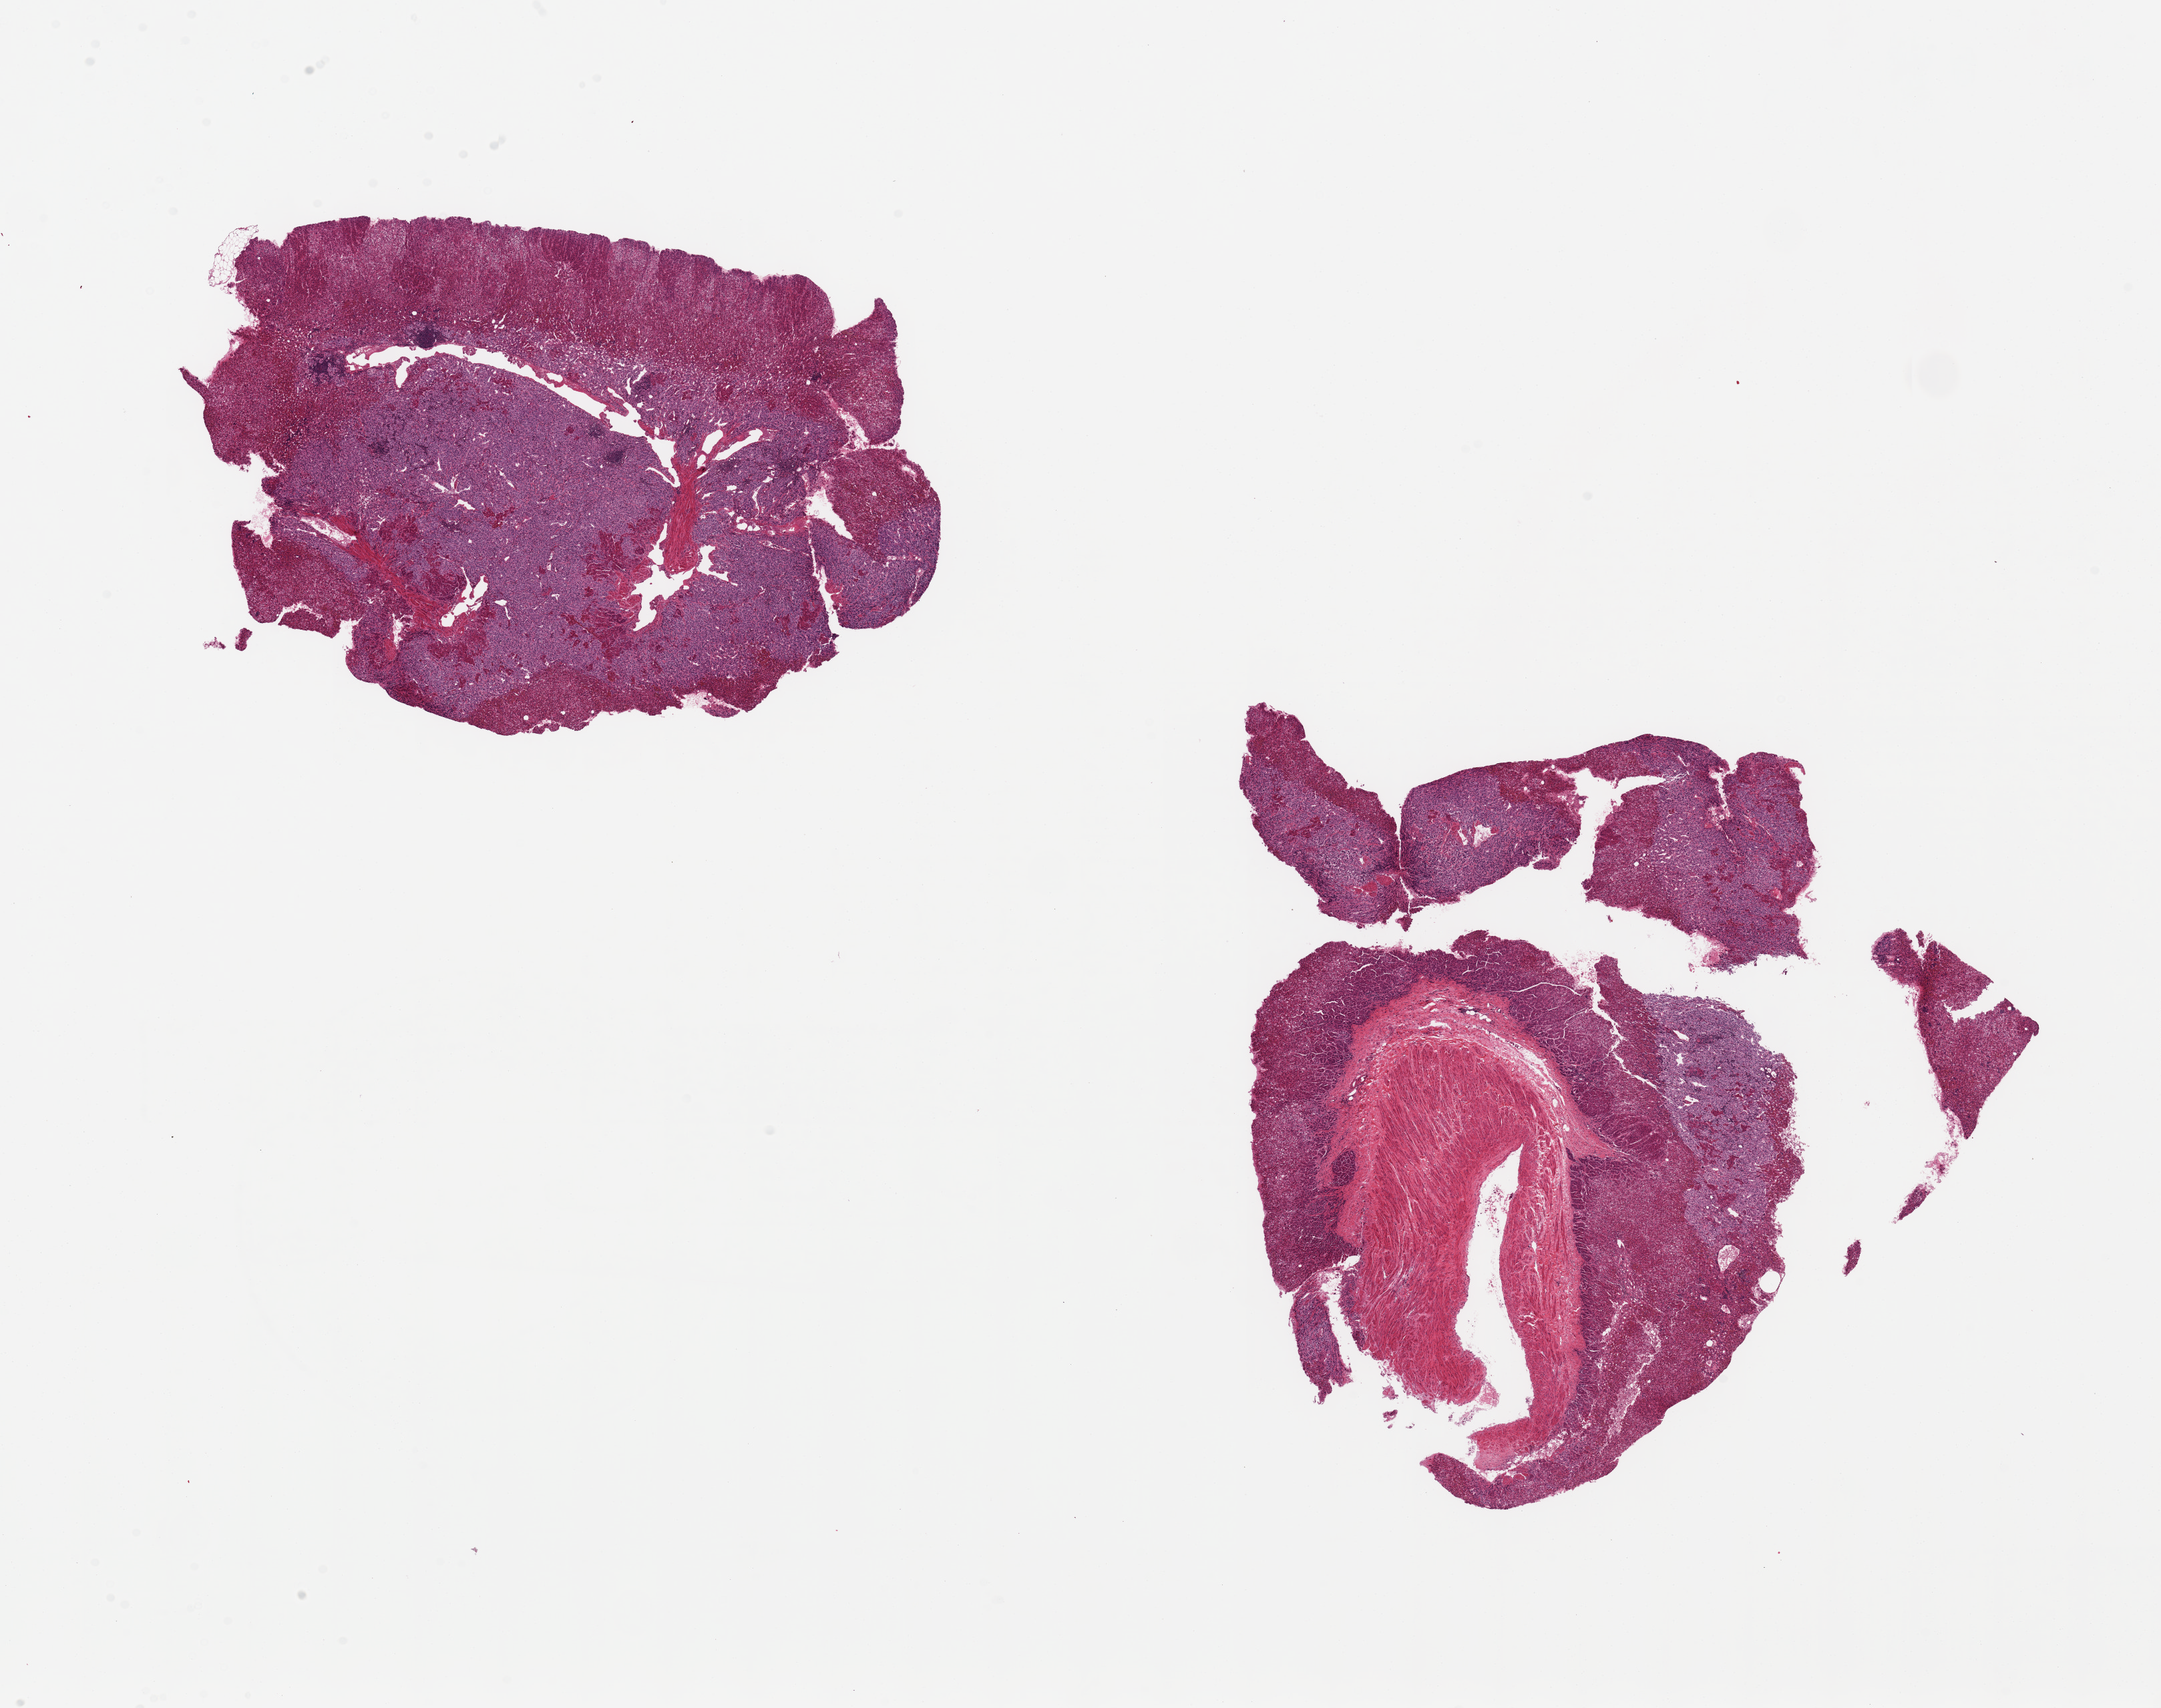
Haematoxylin and eosin whole-slide image — a low-resolution overview of the entire scanned area, about 25.6 x 20.2 mm. PAXgene-fixed, paraffin-embedded tissue. Section of adrenal gland (target tissue). Donor tissue sample. Donor sex: male.
* reviewer comment on this tissue sample: 2 ~ 8x6mm pieces. Both cortex and medulla well-preserved